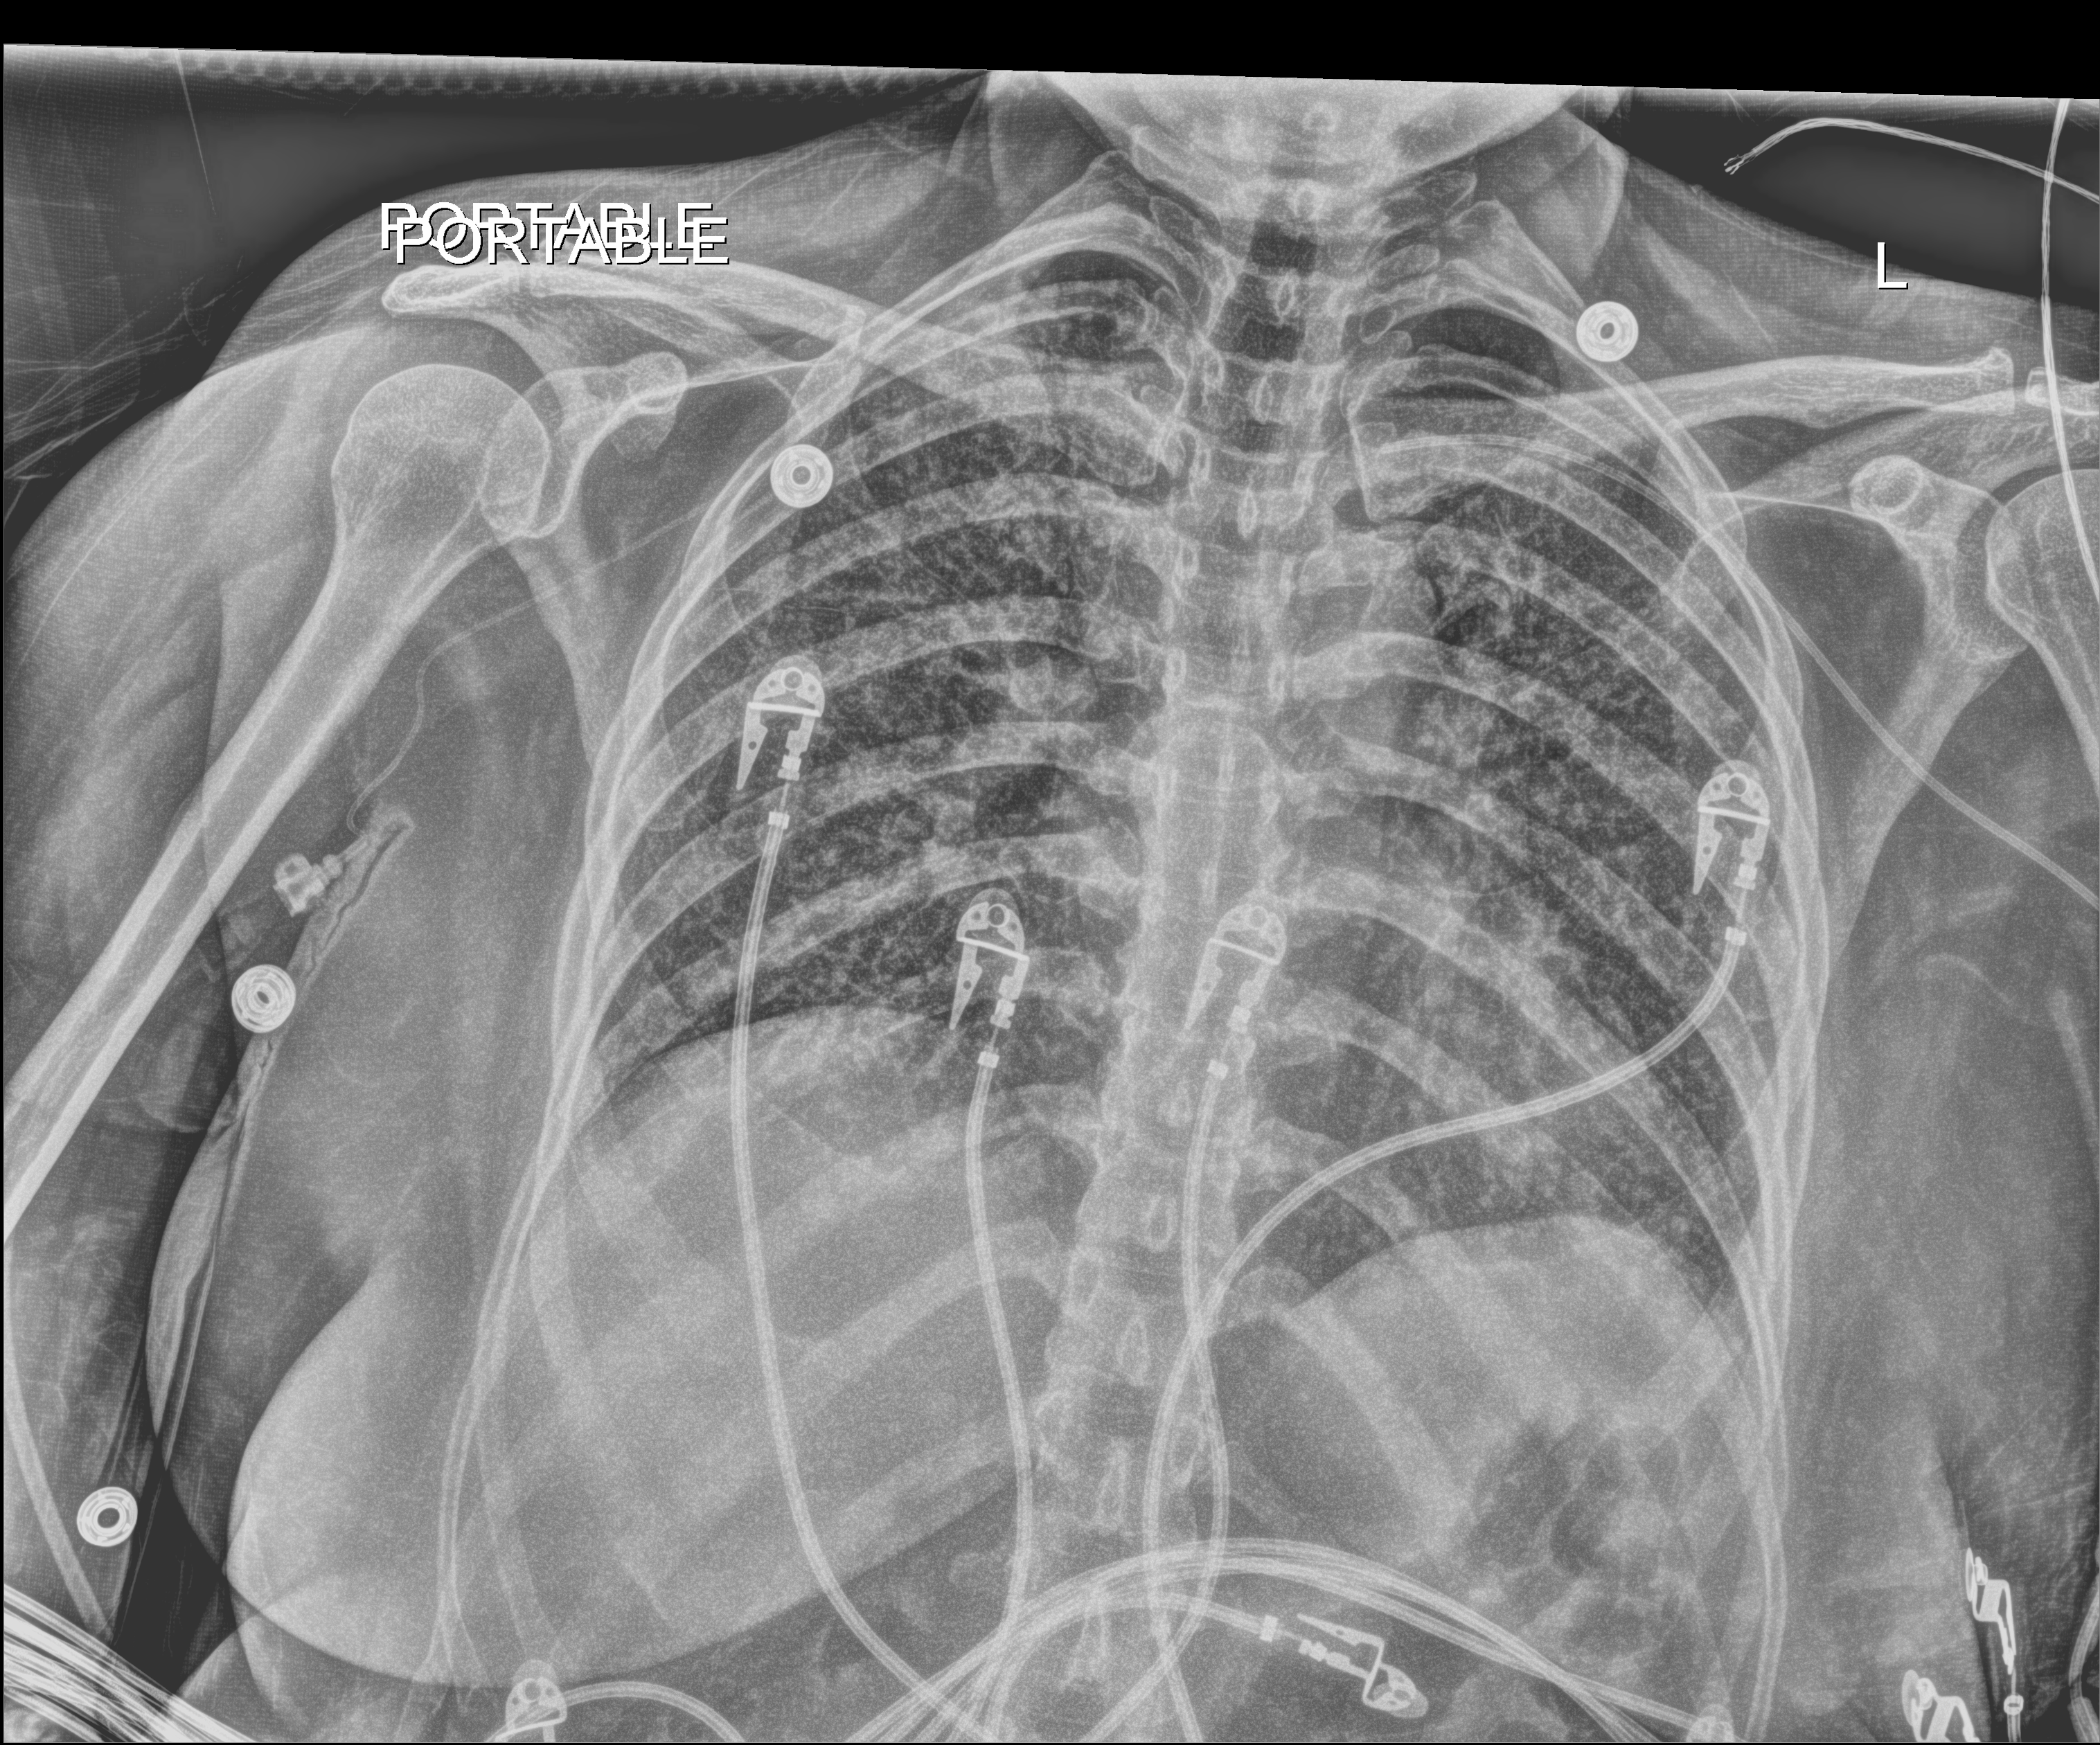
Portable chest radiograph, anteroposterior (AP) projection. Male patient hospitalised with COVID-19, age 18–59 years.
Admission-level facts for this patient (not findings on this image; timing relative to this image not recorded):
- mechanically ventilated during this hospital stay: yes